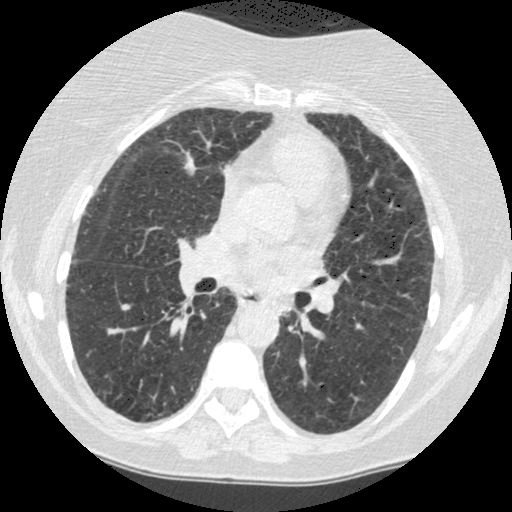
Chest CT (low-dose screening protocol), one axial image; baseline annual screen; lung window (W 1500 / L -600 HU); 1.25 mm slice thickness; standard (soft-tissue) reconstruction kernel (STANDARD); 120 kVp. Female participant, aged 60 years at enrolment. Former smoker at enrolment.
Expert reader's lesion annotation, box from (x=263, y=289) to (x=306, y=330) px. The screening reader recorded 2 non-calcified nodules or masses ≥4 mm on this exam; which of them this box marks is not recorded. Official screen result: positive, change unspecified: nodule(s) >= 4 mm or enlarging nodule(s), mass(es), or other non-specific abnormalities suspicious for lung cancer. Participant outcome: lung cancer diagnosed 794 days after this screen (after the third annual screen) — small cell carcinoma, NOS, left lower lobe, undifferentiated (G4), stage IV (AJCC 6th edition), 69 mm at pathology.